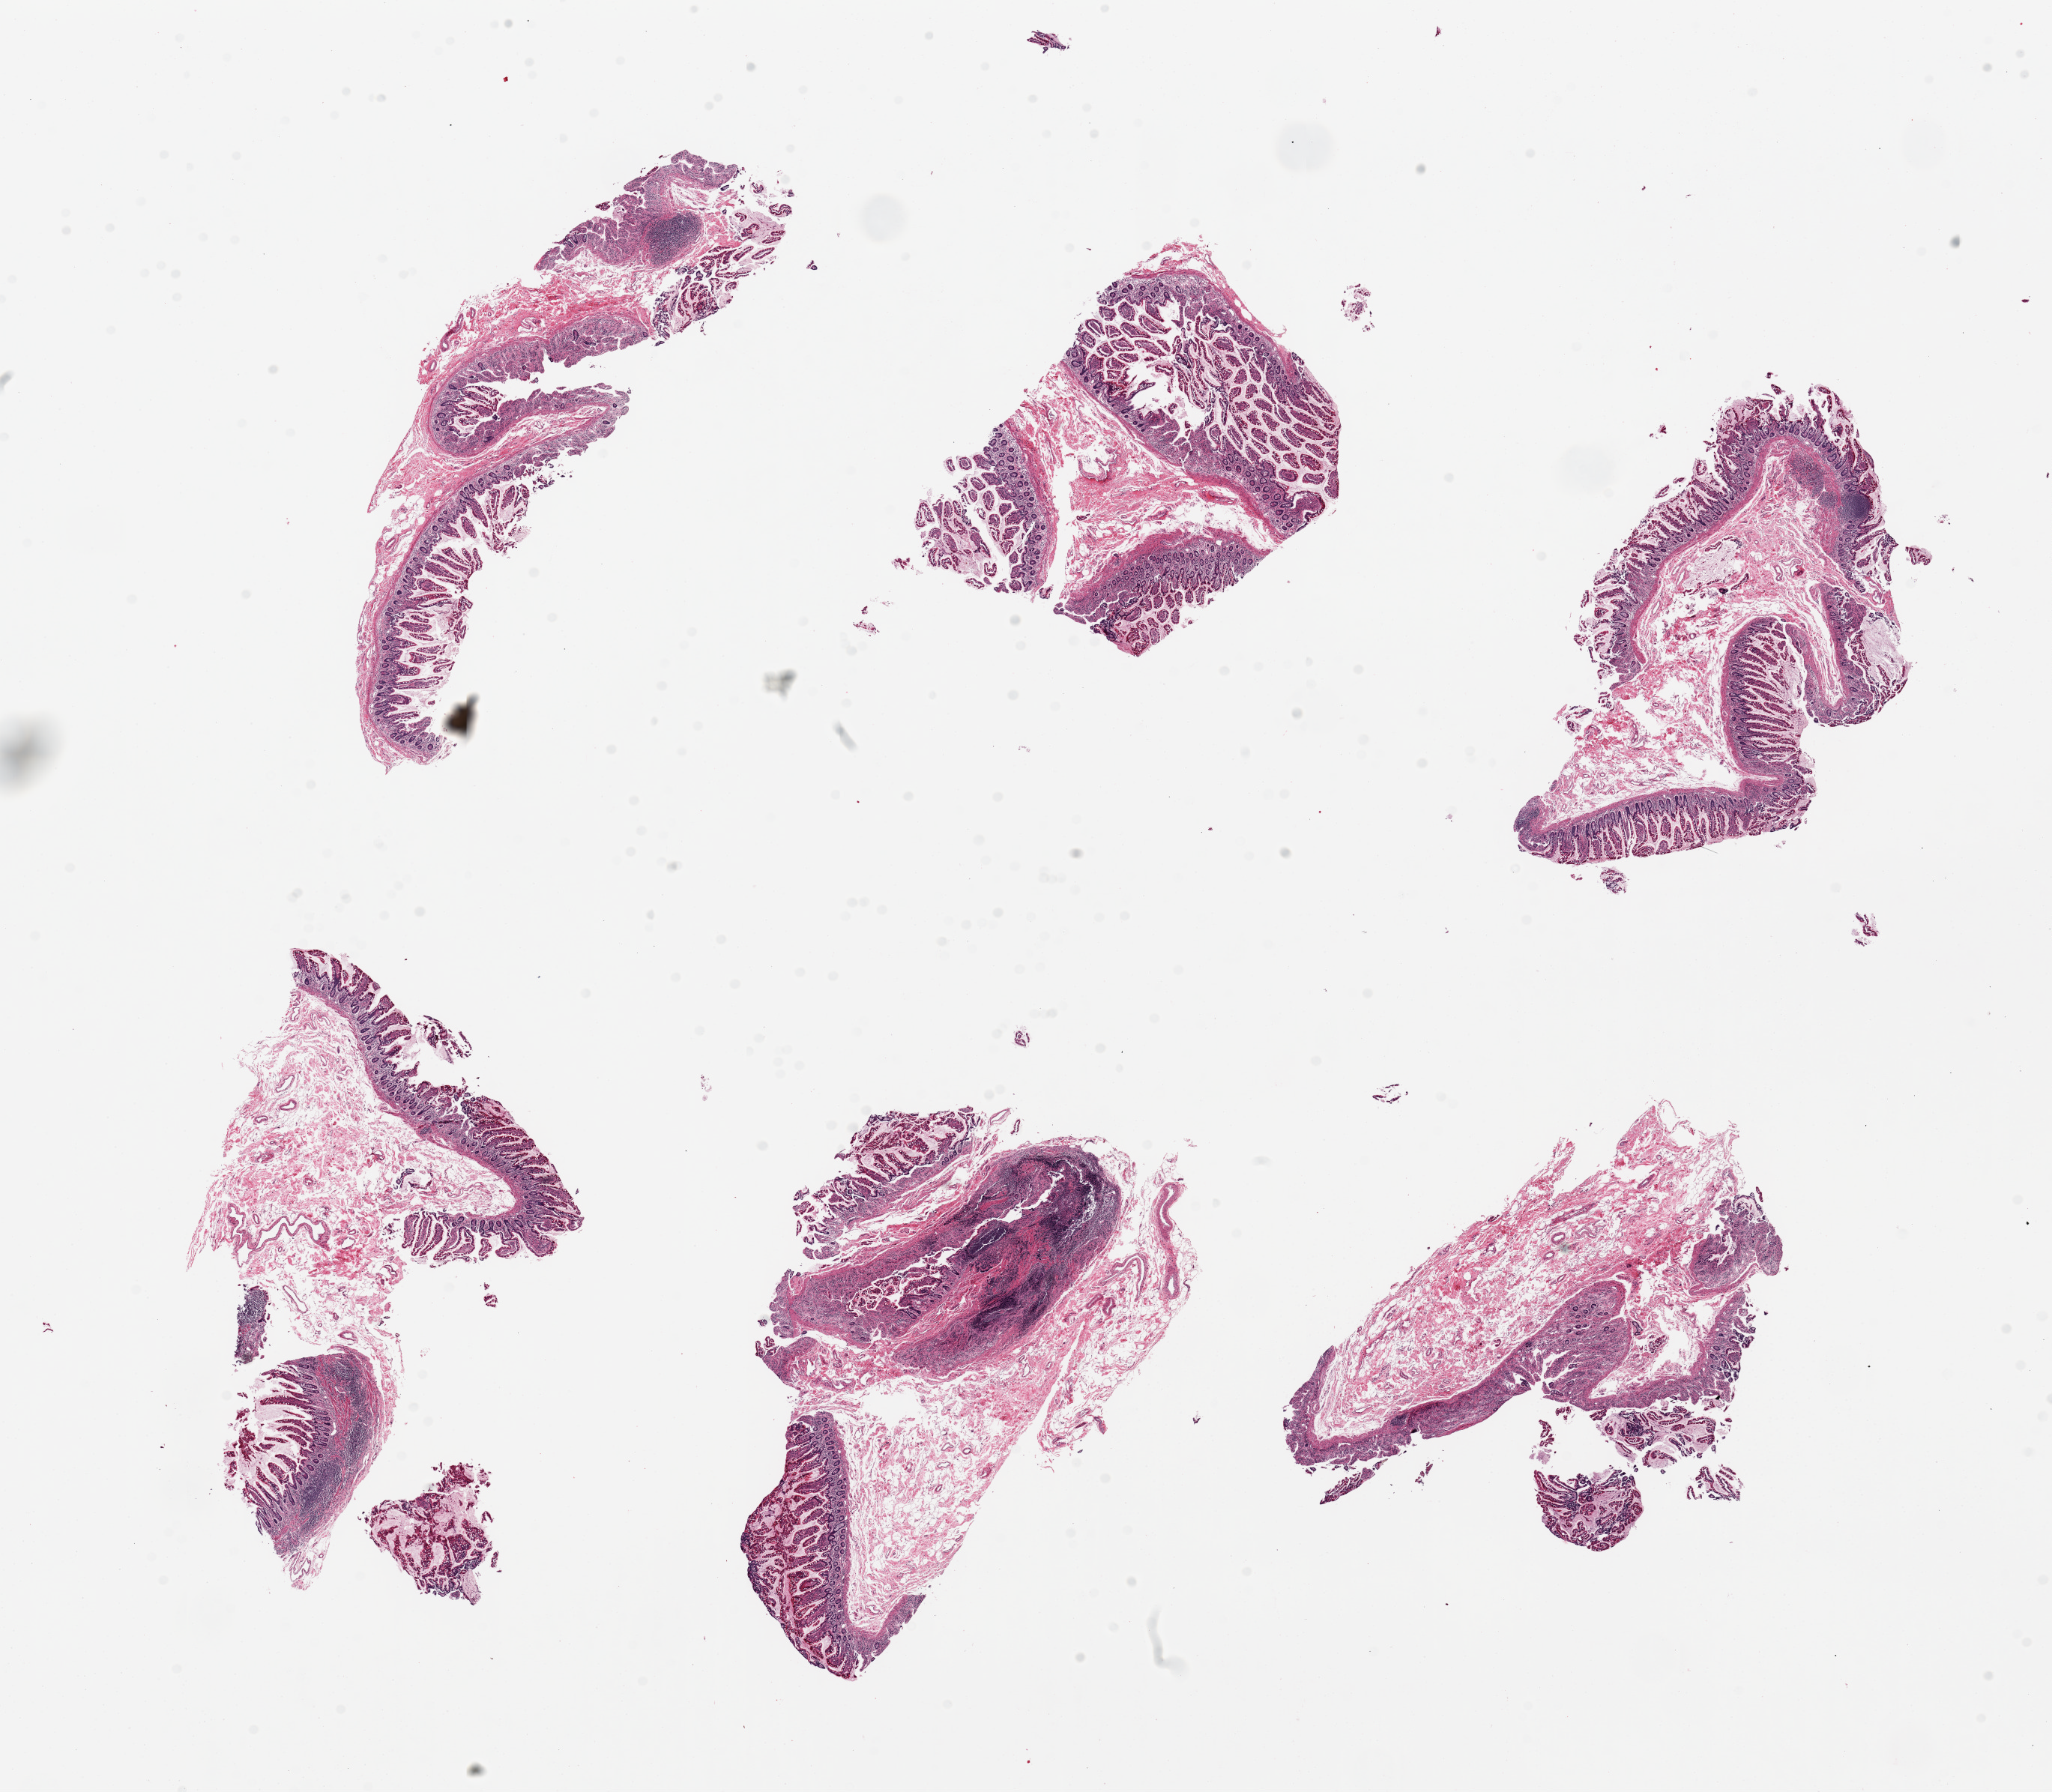
H&E whole-slide image — shown as a low-resolution overview of the whole scanned area (about 21.7 x 18.9 mm, slide scanned at 20x), PAXgene-fixed paraffin-embedded (PFPE) section, section of ileum (target tissue), tissue donor sample.
- pathologist's review note for this sample: 6 pieces, mucosa and stroma, ~5-10% lylmphoid elements